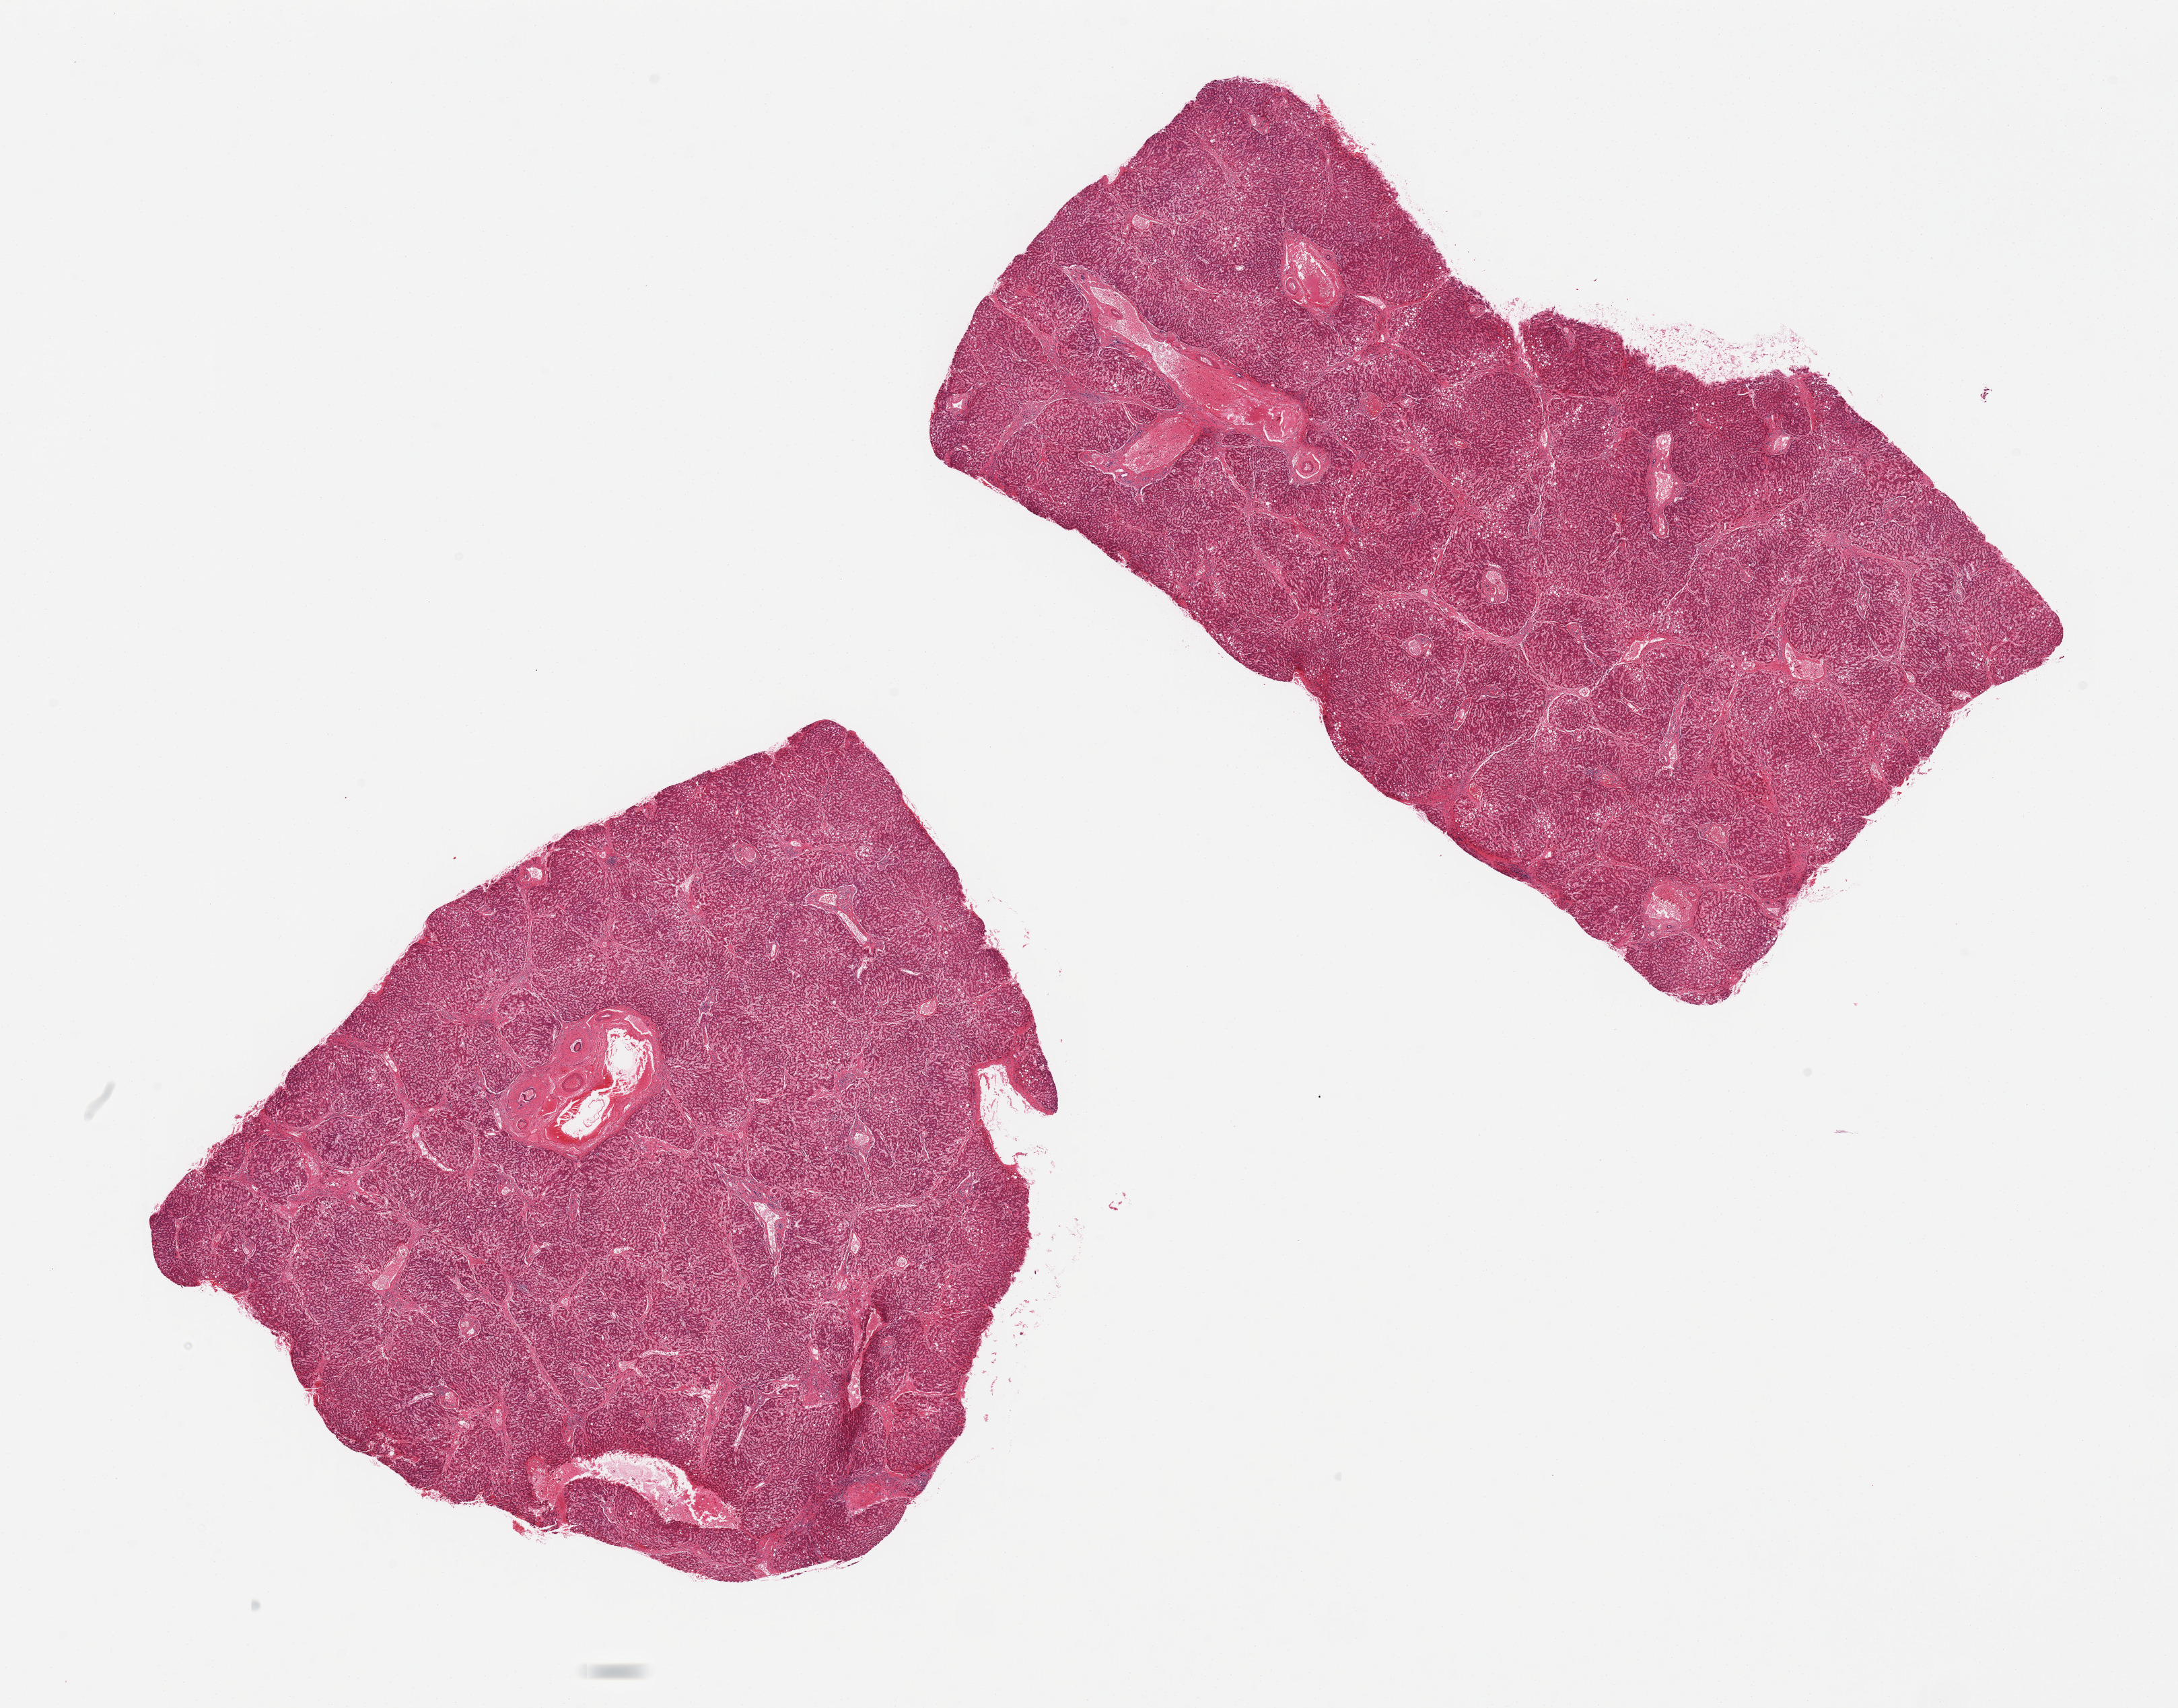
H&E whole-slide image — whole scanned area (about 25.6 x 20.1 mm) shown as a low-resolution overview, PAXgene-fixed paraffin-embedded (PFPE) section, target tissue: liver, tissue donor sample. Male donor.
Review note (as recorded): 2 pieces, passive congestion, bridging fibrosis, some chronic inflammation, mild-moderate steatosis.